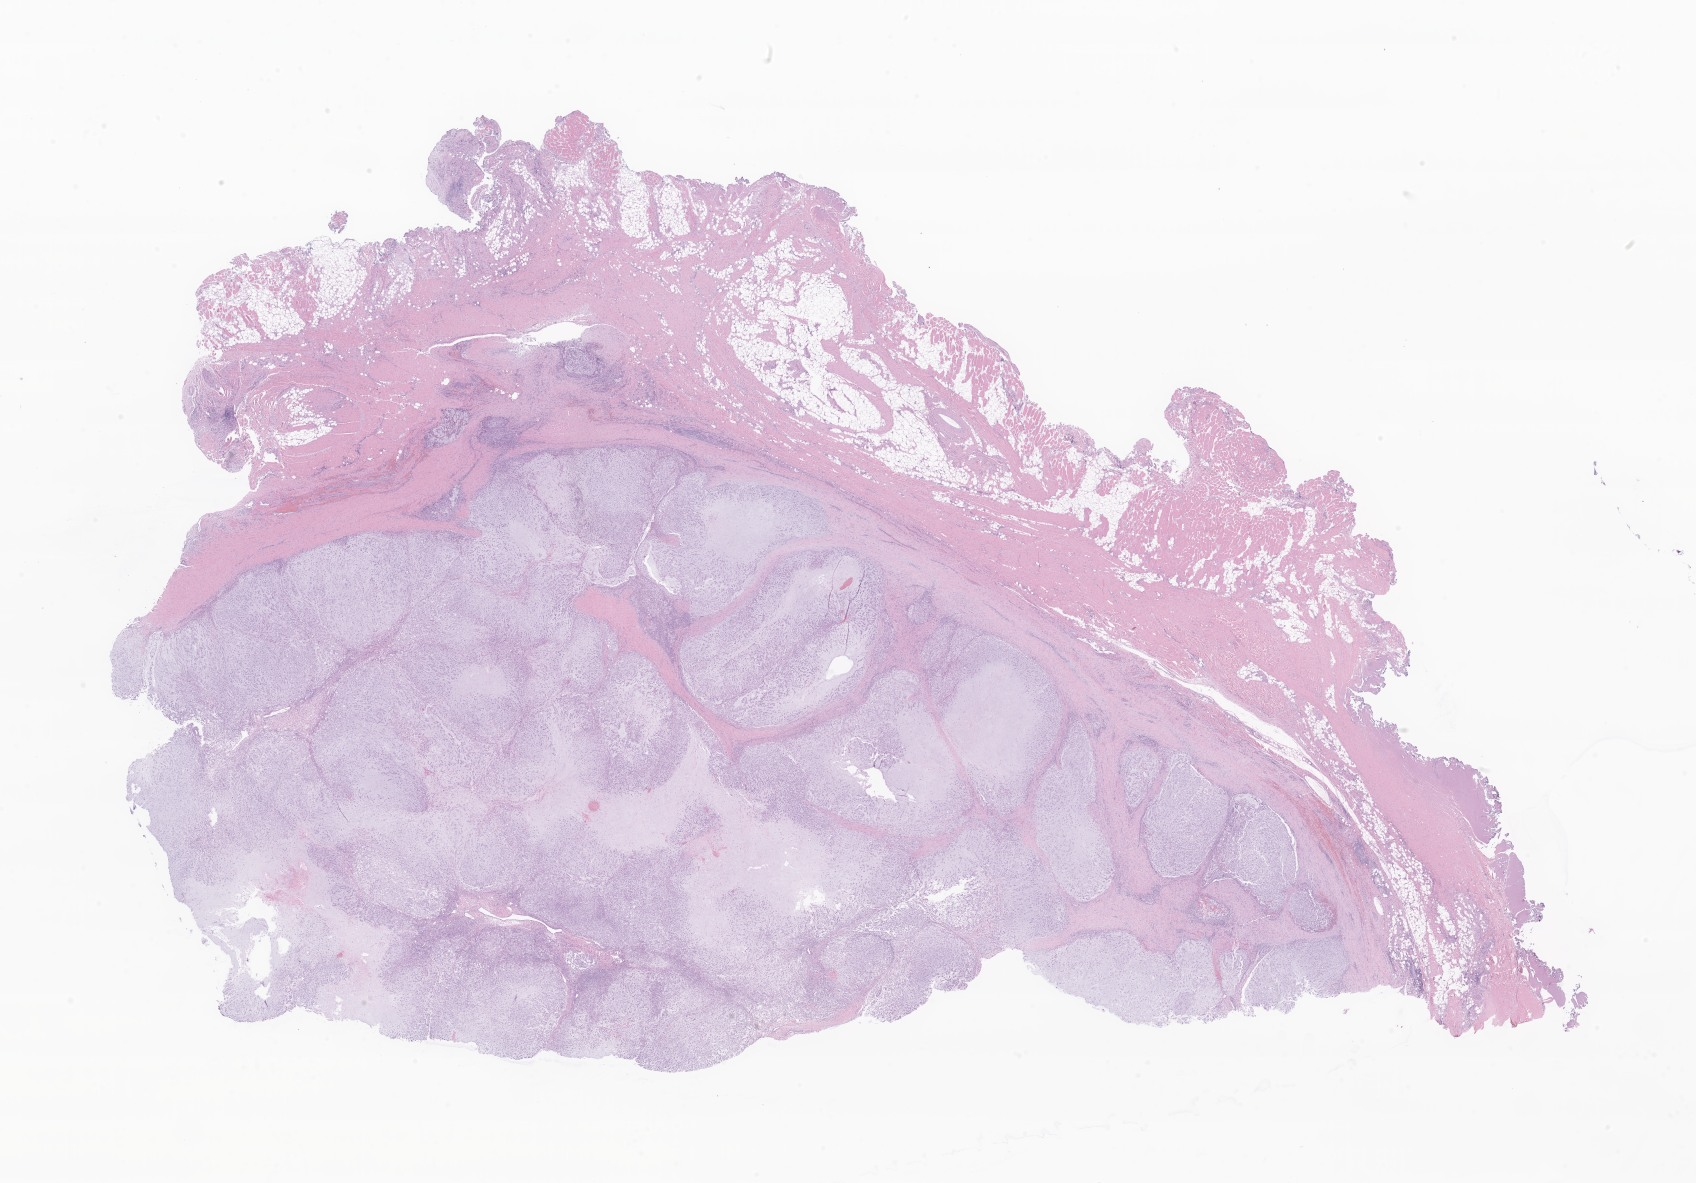
H&E whole-slide image of tumor tissue from the innominate bone and/or sacrum and/or coccyx, whole scanned area (about 28.6 x 20.0 mm) shown as a low-resolution overview; formalin-fixed, paraffin-embedded (FFPE) tissue. Patient: female, age 92 months (7 years 8 months).
Diagnosis: Chordoma, NOS.